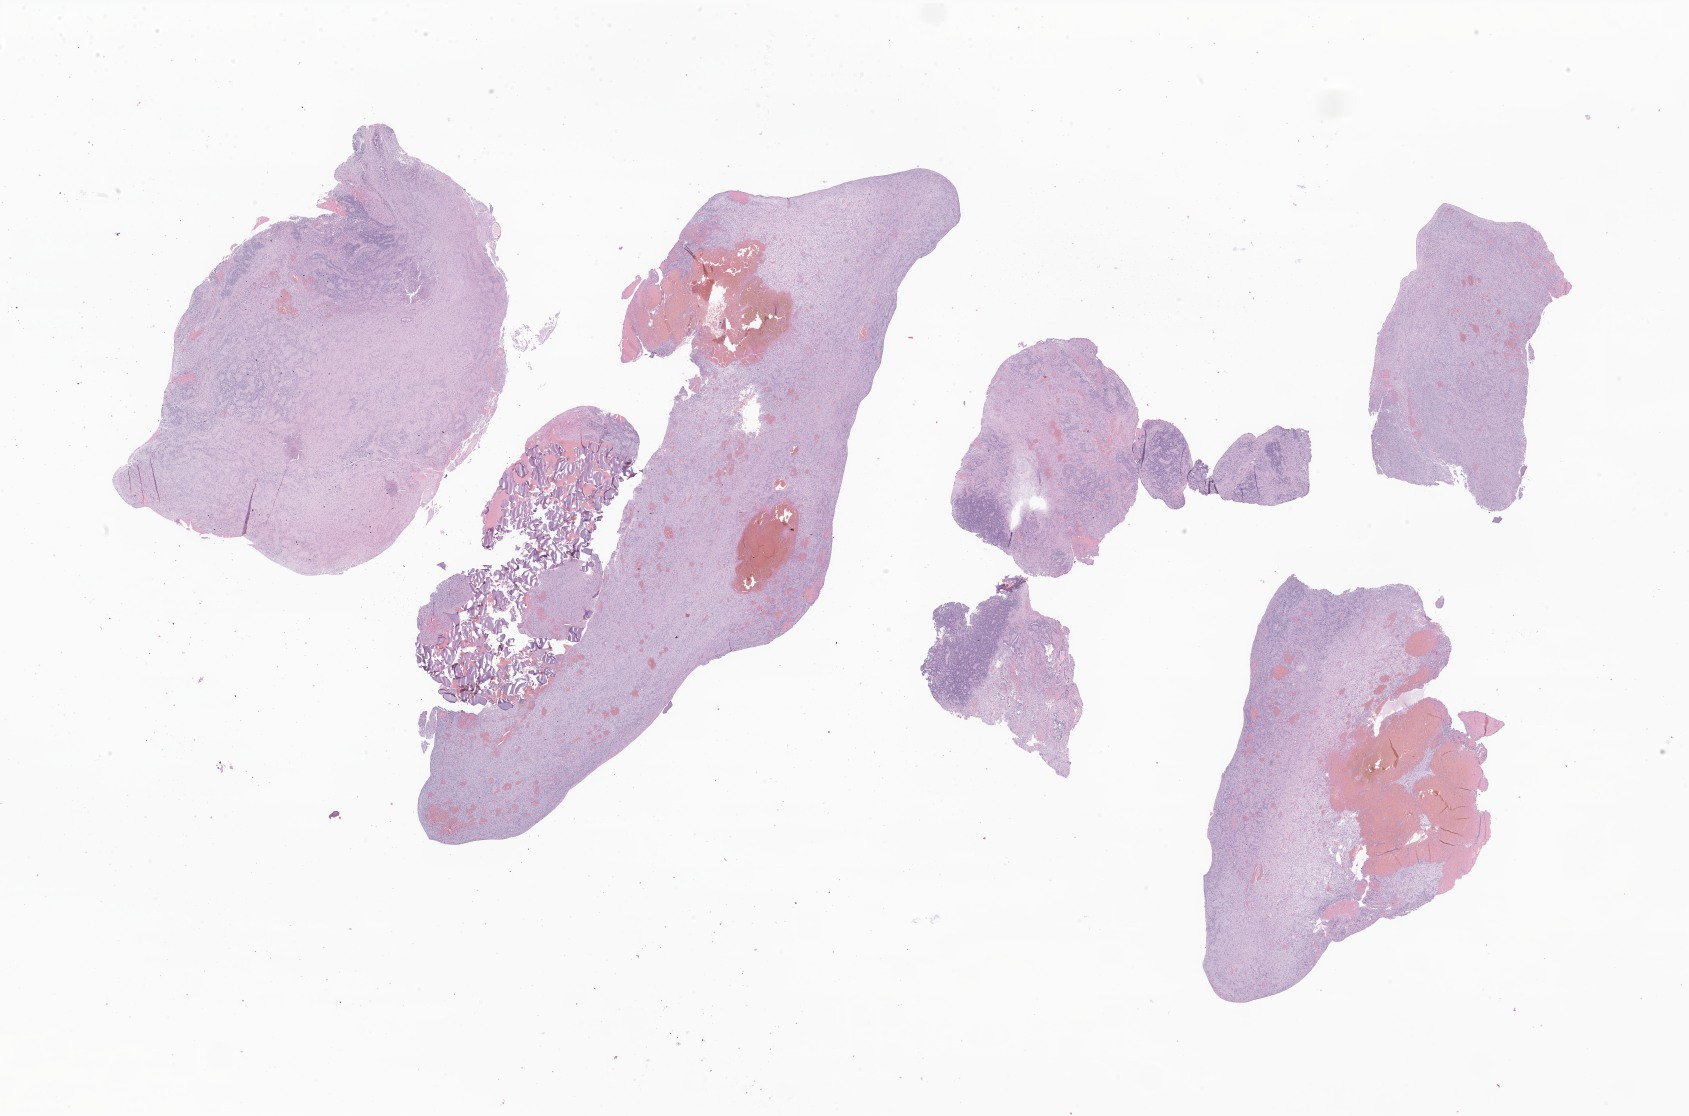
Digitized hematoxylin and eosin (H&E)-stained section of tumor tissue from the brain stem, shown as a low-resolution overview of the whole scanned area (about 28.5 x 18.8 mm), formalin-fixed paraffin-embedded section. Patient: male, age 679 days (about 1.9 years).
* diagnosis (ICD-O-3 morphology term): Ependymoma, NOS